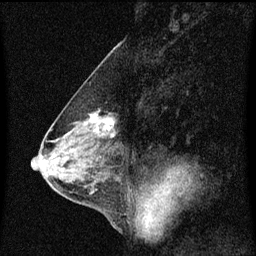
Breast MRI (dynamic contrast-enhanced), one sagittal slice. Slice 33 of 60 in the series (ordered by position). Dynamic contrast-enhanced series, image 2 of 3 at this slice position (ordered by acquisition). 1.5 T. TE 4.2 ms, TR 8.4 ms. 2 mm slice thickness. 256 × 256 image matrix, field of view 200 × 200 mm. Female patient, age 58 years.
Annotated regions visible in this slice (semi-automatic segmentation, software-assisted and operator-edited):
- analysis volume of interest (the breast-tissue region the enhancement analysis was run in; not a lesion): bounding box (x1, y1, x2, y2) in pixels: (79, 108, 120, 143)
- tumour enhancement mask (voxels above the 70 % enhancement threshold inside the analysis volume of interest): (91, 114, 116, 137)